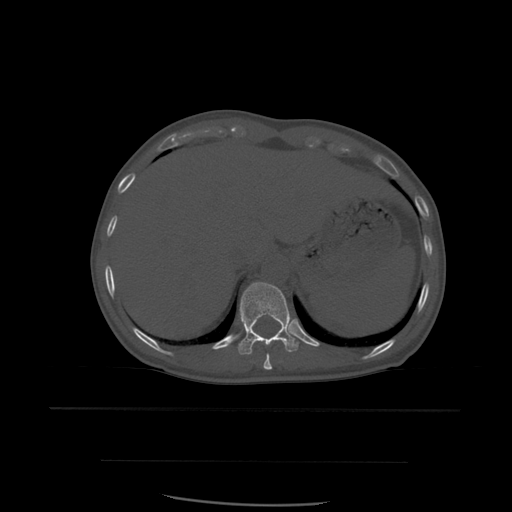
CT including the spine, one axial slice; position 298 of 574 along the scan axis; bone window (W 1800 / L 400 HU); 1.25 mm slice thickness; 512 × 512 image matrix. Patient age 48 years. Case-level facts recorded for this patient, not image findings: primary cancer: lung.
Structures marked on this image (semi-automatic segmentation, software-assisted and operator-edited):
- T10 vertebra: box from (x=263, y=346) to (x=287, y=370) px
- T11 vertebra: (x=238, y=282)–(x=299, y=355)